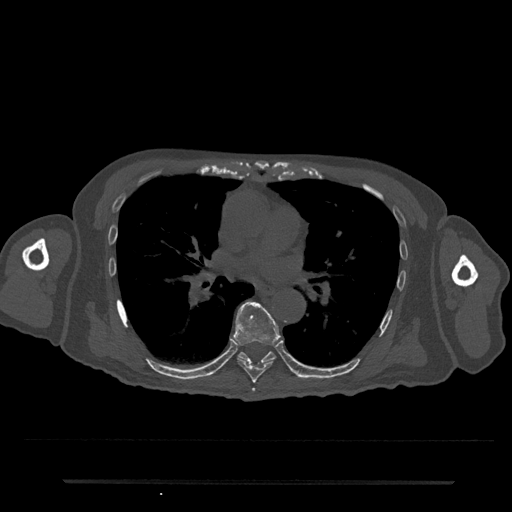
CT including the spine, one axial slice. Slice 459 of 797 in the series (ordered by position). 120 kVp. Bone window (W 1800 / L 400 HU). 512 × 512 image matrix. Male patient, age 74 years. Case-level facts recorded for this patient, not image findings: primary cancer: prostate.
Structures marked on this image (semi-automatic segmentation, software-assisted and operator-edited):
- T6 vertebra: bounding box (x1, y1, x2, y2) in pixels: (252, 388, 255, 392)
- T7 vertebra: (233, 301, 281, 383)
- T8 vertebra: (237, 352, 276, 365)